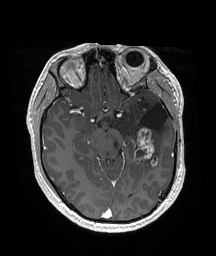
Brain MRI from a brain-tumour surgery series, one axial slice; slice 106 of 192 in the series (ordered by position); T1-weighted post-contrast; 1 mm slice thickness; 216 × 256 image matrix. Case-level facts recorded for this patient, not image findings: histopathology: Glioneuronal tumor; WHO grade: 2.
Structures marked on this image (manually delineated by an expert):
- previous resection cavity: bounding box [x1, y1, x2, y2] px = [139, 103, 168, 131]
- tumour: [133, 108, 159, 166]